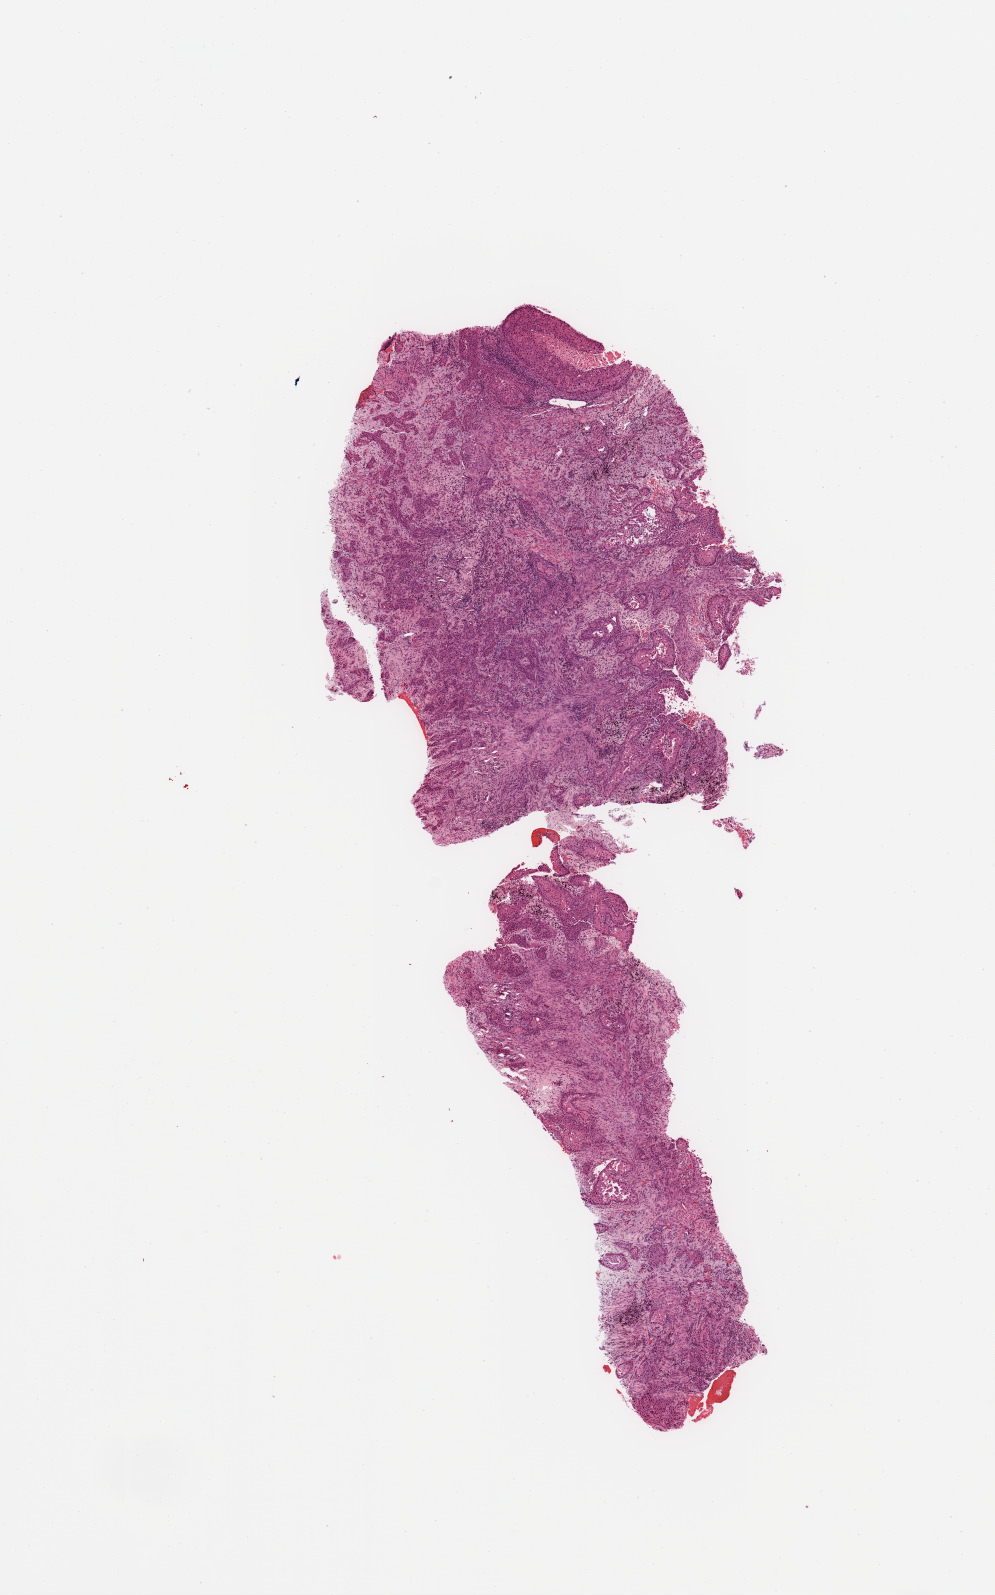
Whole-slide histology image, Hematoxylin and eosin (H&E) stained, low-resolution overview of the scanned area, about 7.9 x 12.6 mm, lung, tumour tissue. Male, 70 y/o. Histologic grade: G2 (moderately differentiated).
AJCC pathologic stage: IB. Diagnosis: Squamous cell carcinoma, NOS. Primary tumour site (as recorded): right upper lobe.